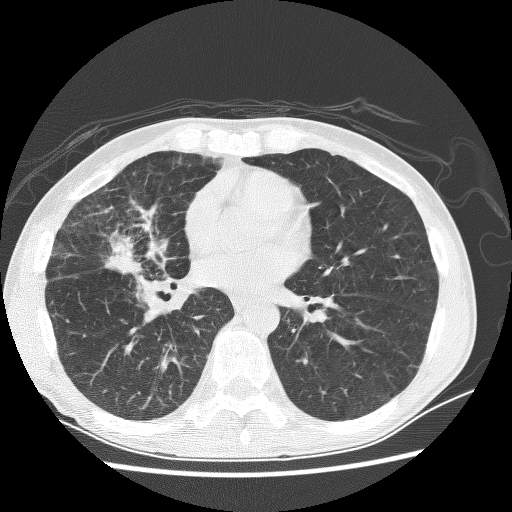
Axial slice from a low-dose chest CT screening exam, baseline annual screen, lung window (W 1500 / L -600 HU), 2.5 mm slice thickness, lung (sharp) reconstruction kernel (BONE), slice 139 of 256 in the series, 512 × 512 image matrix. Male, age 67 years at enrolment. Current smoker at enrolment.
Expert-annotated lung lesion, bounding box [x1, y1, x2, y2] px = [81, 217, 174, 288]. The exam's reader record, not a measurement of the box and not confirmed to be the same lesion: non-calcified nodule or mass ≥4 mm, right middle lobe, 28 × 18 mm, spiculated (stellate) margins, soft tissue attenuation. Participant outcome: lung cancer diagnosed 69 days after this screen — adenocarcinoma, NOS, right middle lobe, stage IV (AJCC 6th edition), 60 mm at pathology.